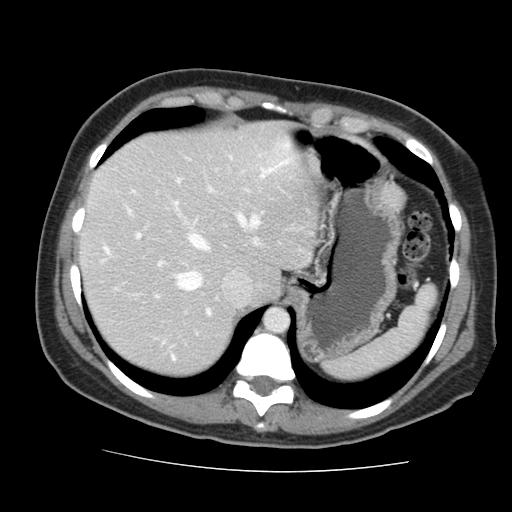
Contrast-enhanced abdominal CT, one axial slice; position 118 of 144 along the scan axis; soft-tissue window (W 400 / L 40 HU); 2.5 mm slice thickness; 512 × 512 image matrix, field of view 333 × 333 mm. Female patient, age 46 years. From the clinical record (not read from this slice): diagnosis: colorectal cancer liver metastases, imaged before liver resection.
Annotated regions visible in this slice (outlined manually by an expert reader):
- hepatic veins: bounding box (x1, y1, x2, y2) in pixels: (104, 169, 272, 291)
- liver: (82, 127, 318, 374)
- planned liver remnant (the part of the liver to remain after resection): (82, 127, 318, 374)
- portal vein (with intrahepatic branches): (127, 179, 213, 359)